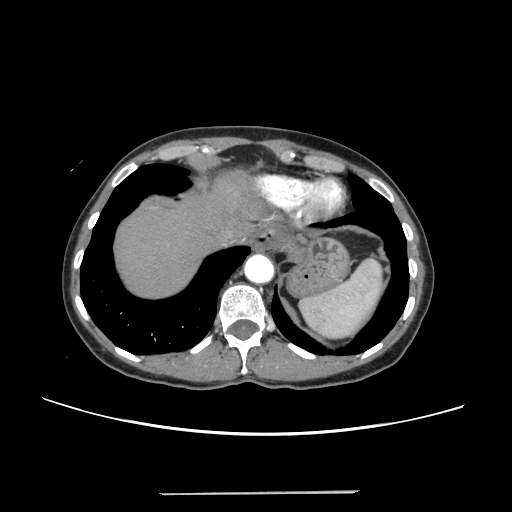
Contrast-enhanced abdominal CT, one axial slice. Slice 213 of 240 in the series (ordered by position). Intravenous contrast given. Soft-tissue window (W 400 / L 40 HU). 512 × 512 image matrix, field of view 371 × 371 mm. Female patient, age 60 years. Case-level facts recorded for this patient, not image findings: diagnosis: colorectal cancer liver metastases, imaged before liver resection; multiple liver metastases: no; largest metastasis: 1.5 cm.
Annotated regions visible in this slice (manually delineated by an expert):
- hepatic veins: bounding box <225,232,231,238> (left, top, right, bottom; pixels)
- liver: <115,175,317,298>
- planned liver remnant (the part of the liver to remain after resection): <115,175,251,298>